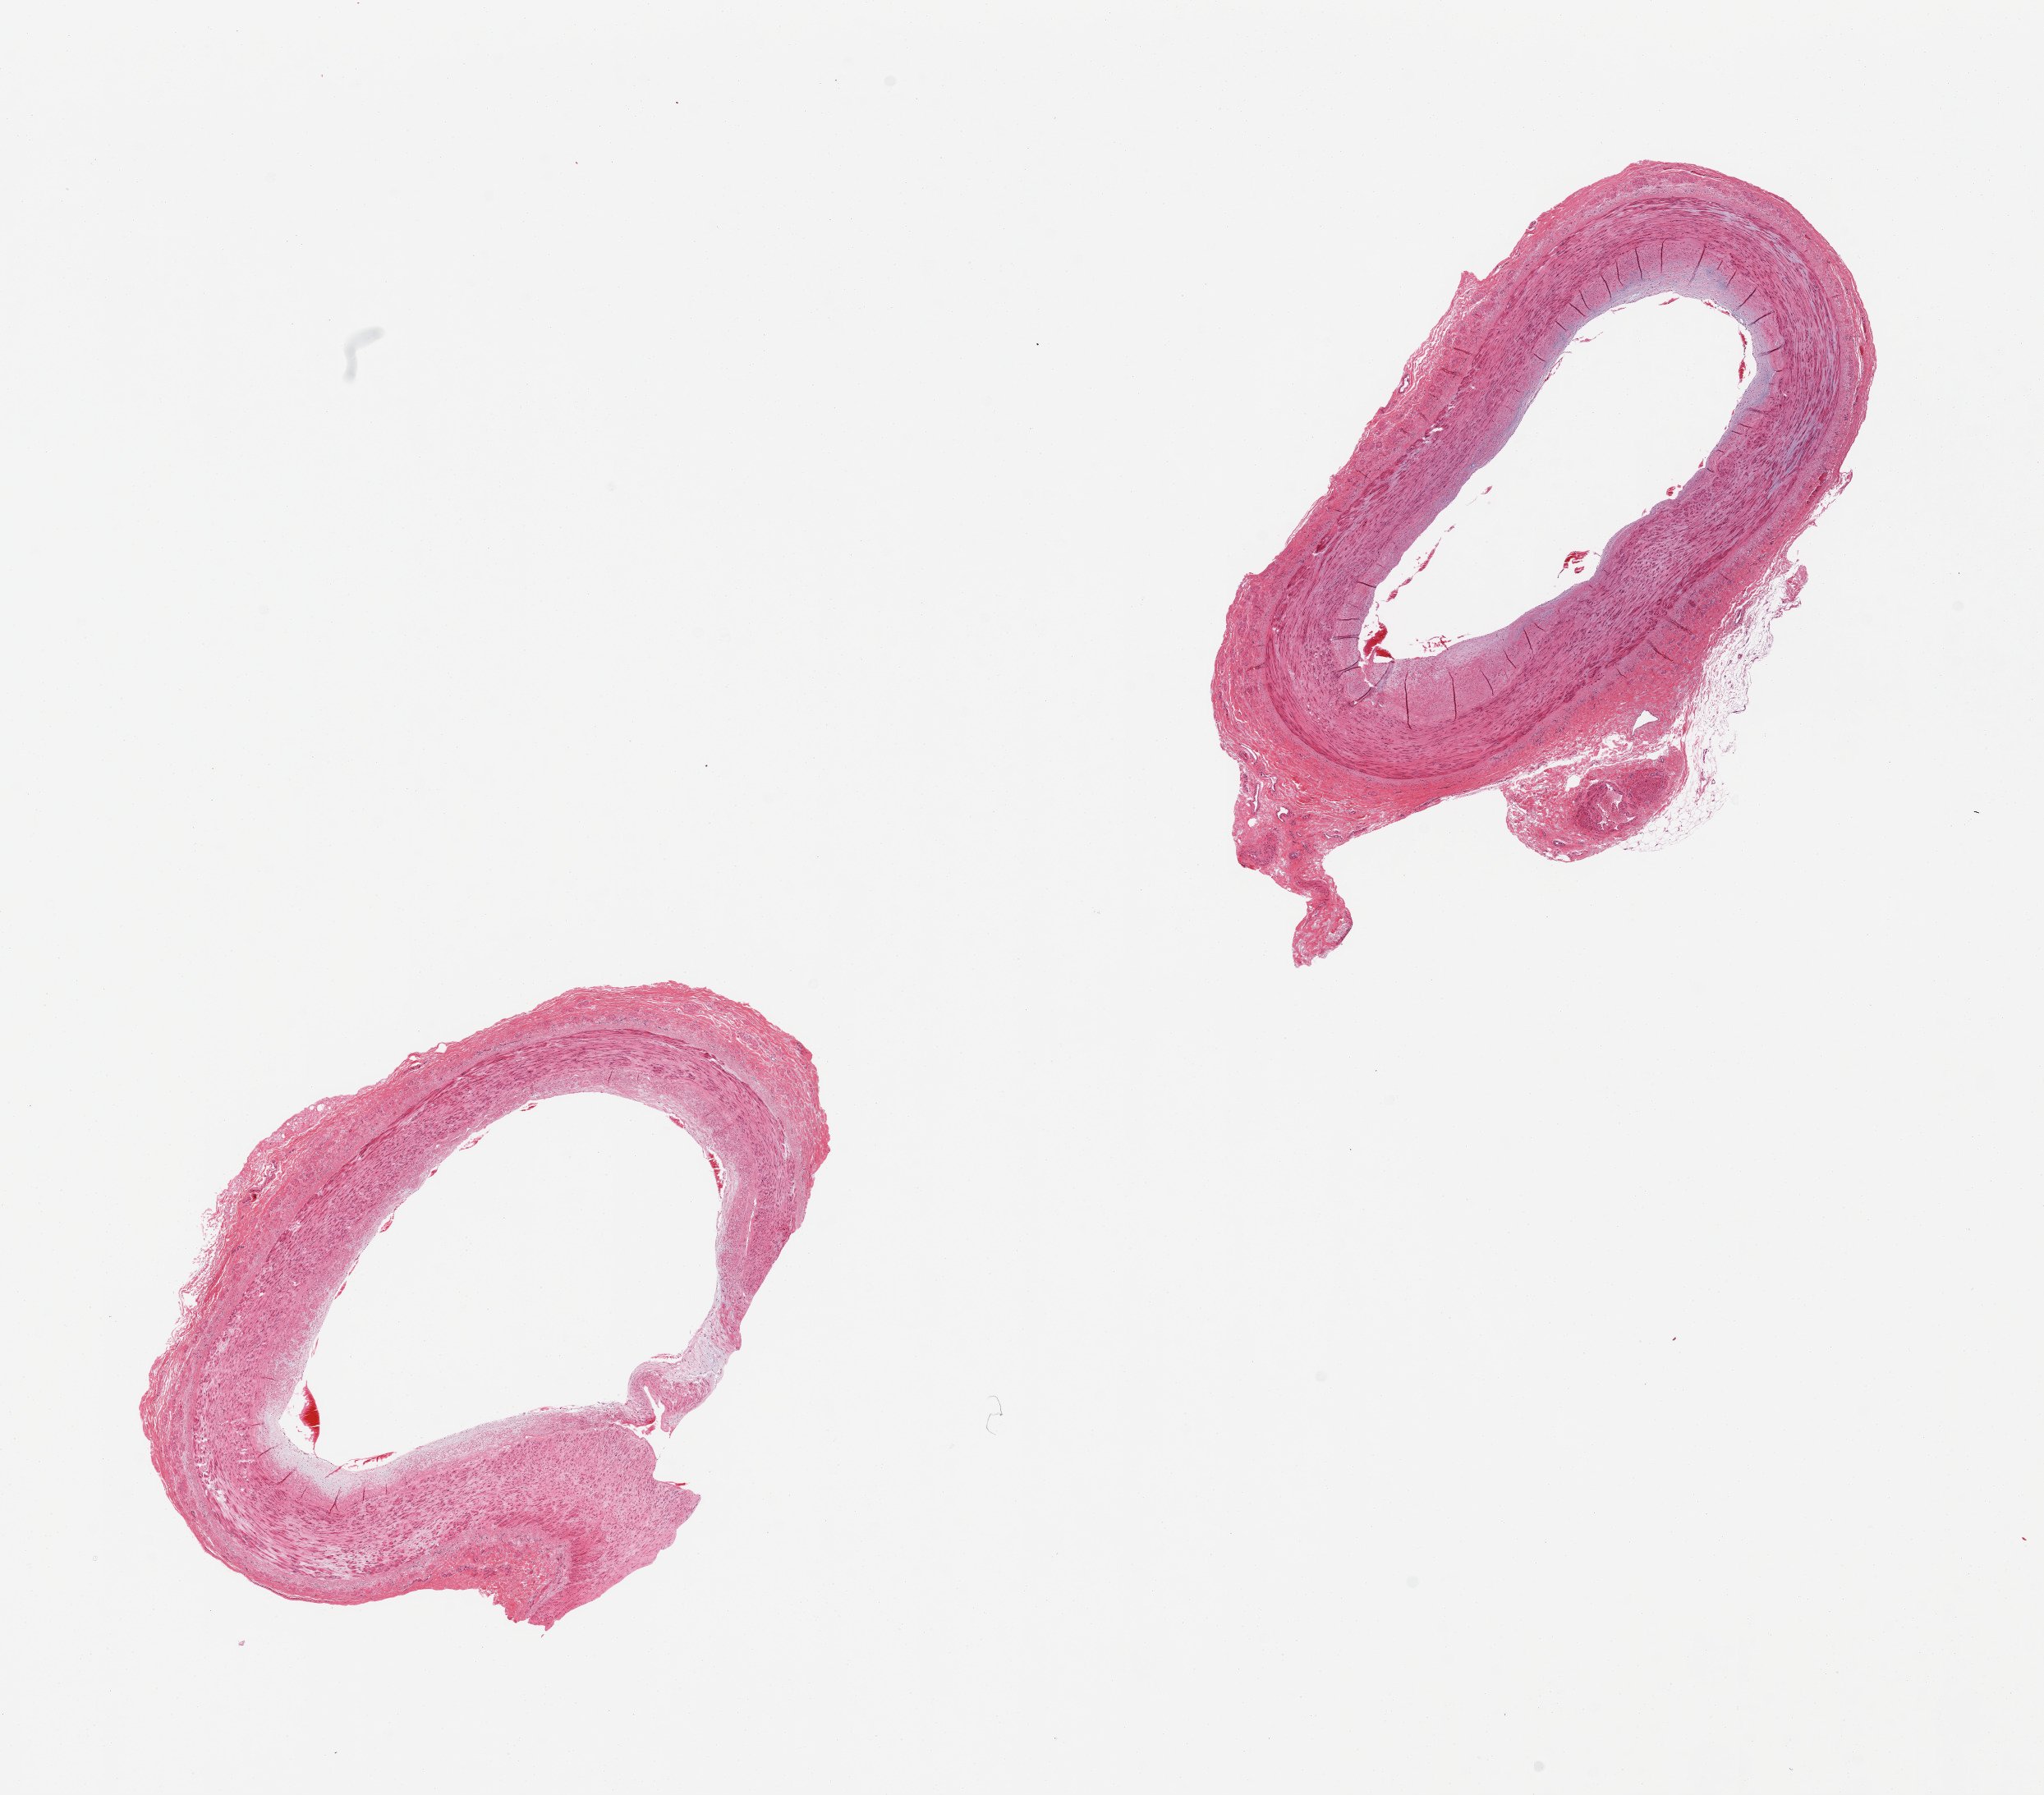
Whole-slide image, hematoxylin and eosin (H&E) stain, brightfield, shown as a low-resolution overview of the whole scanned area (about 19.7 x 17.3 mm, from a 20x scan). PAXgene-fixed paraffin-embedded (PFPE) section. Sampled site (target tissue): tibial artery. Tissue donor sample.
Review note (as recorded): 2 pieces, focal adherent fibrous tissue, good clean specimens.